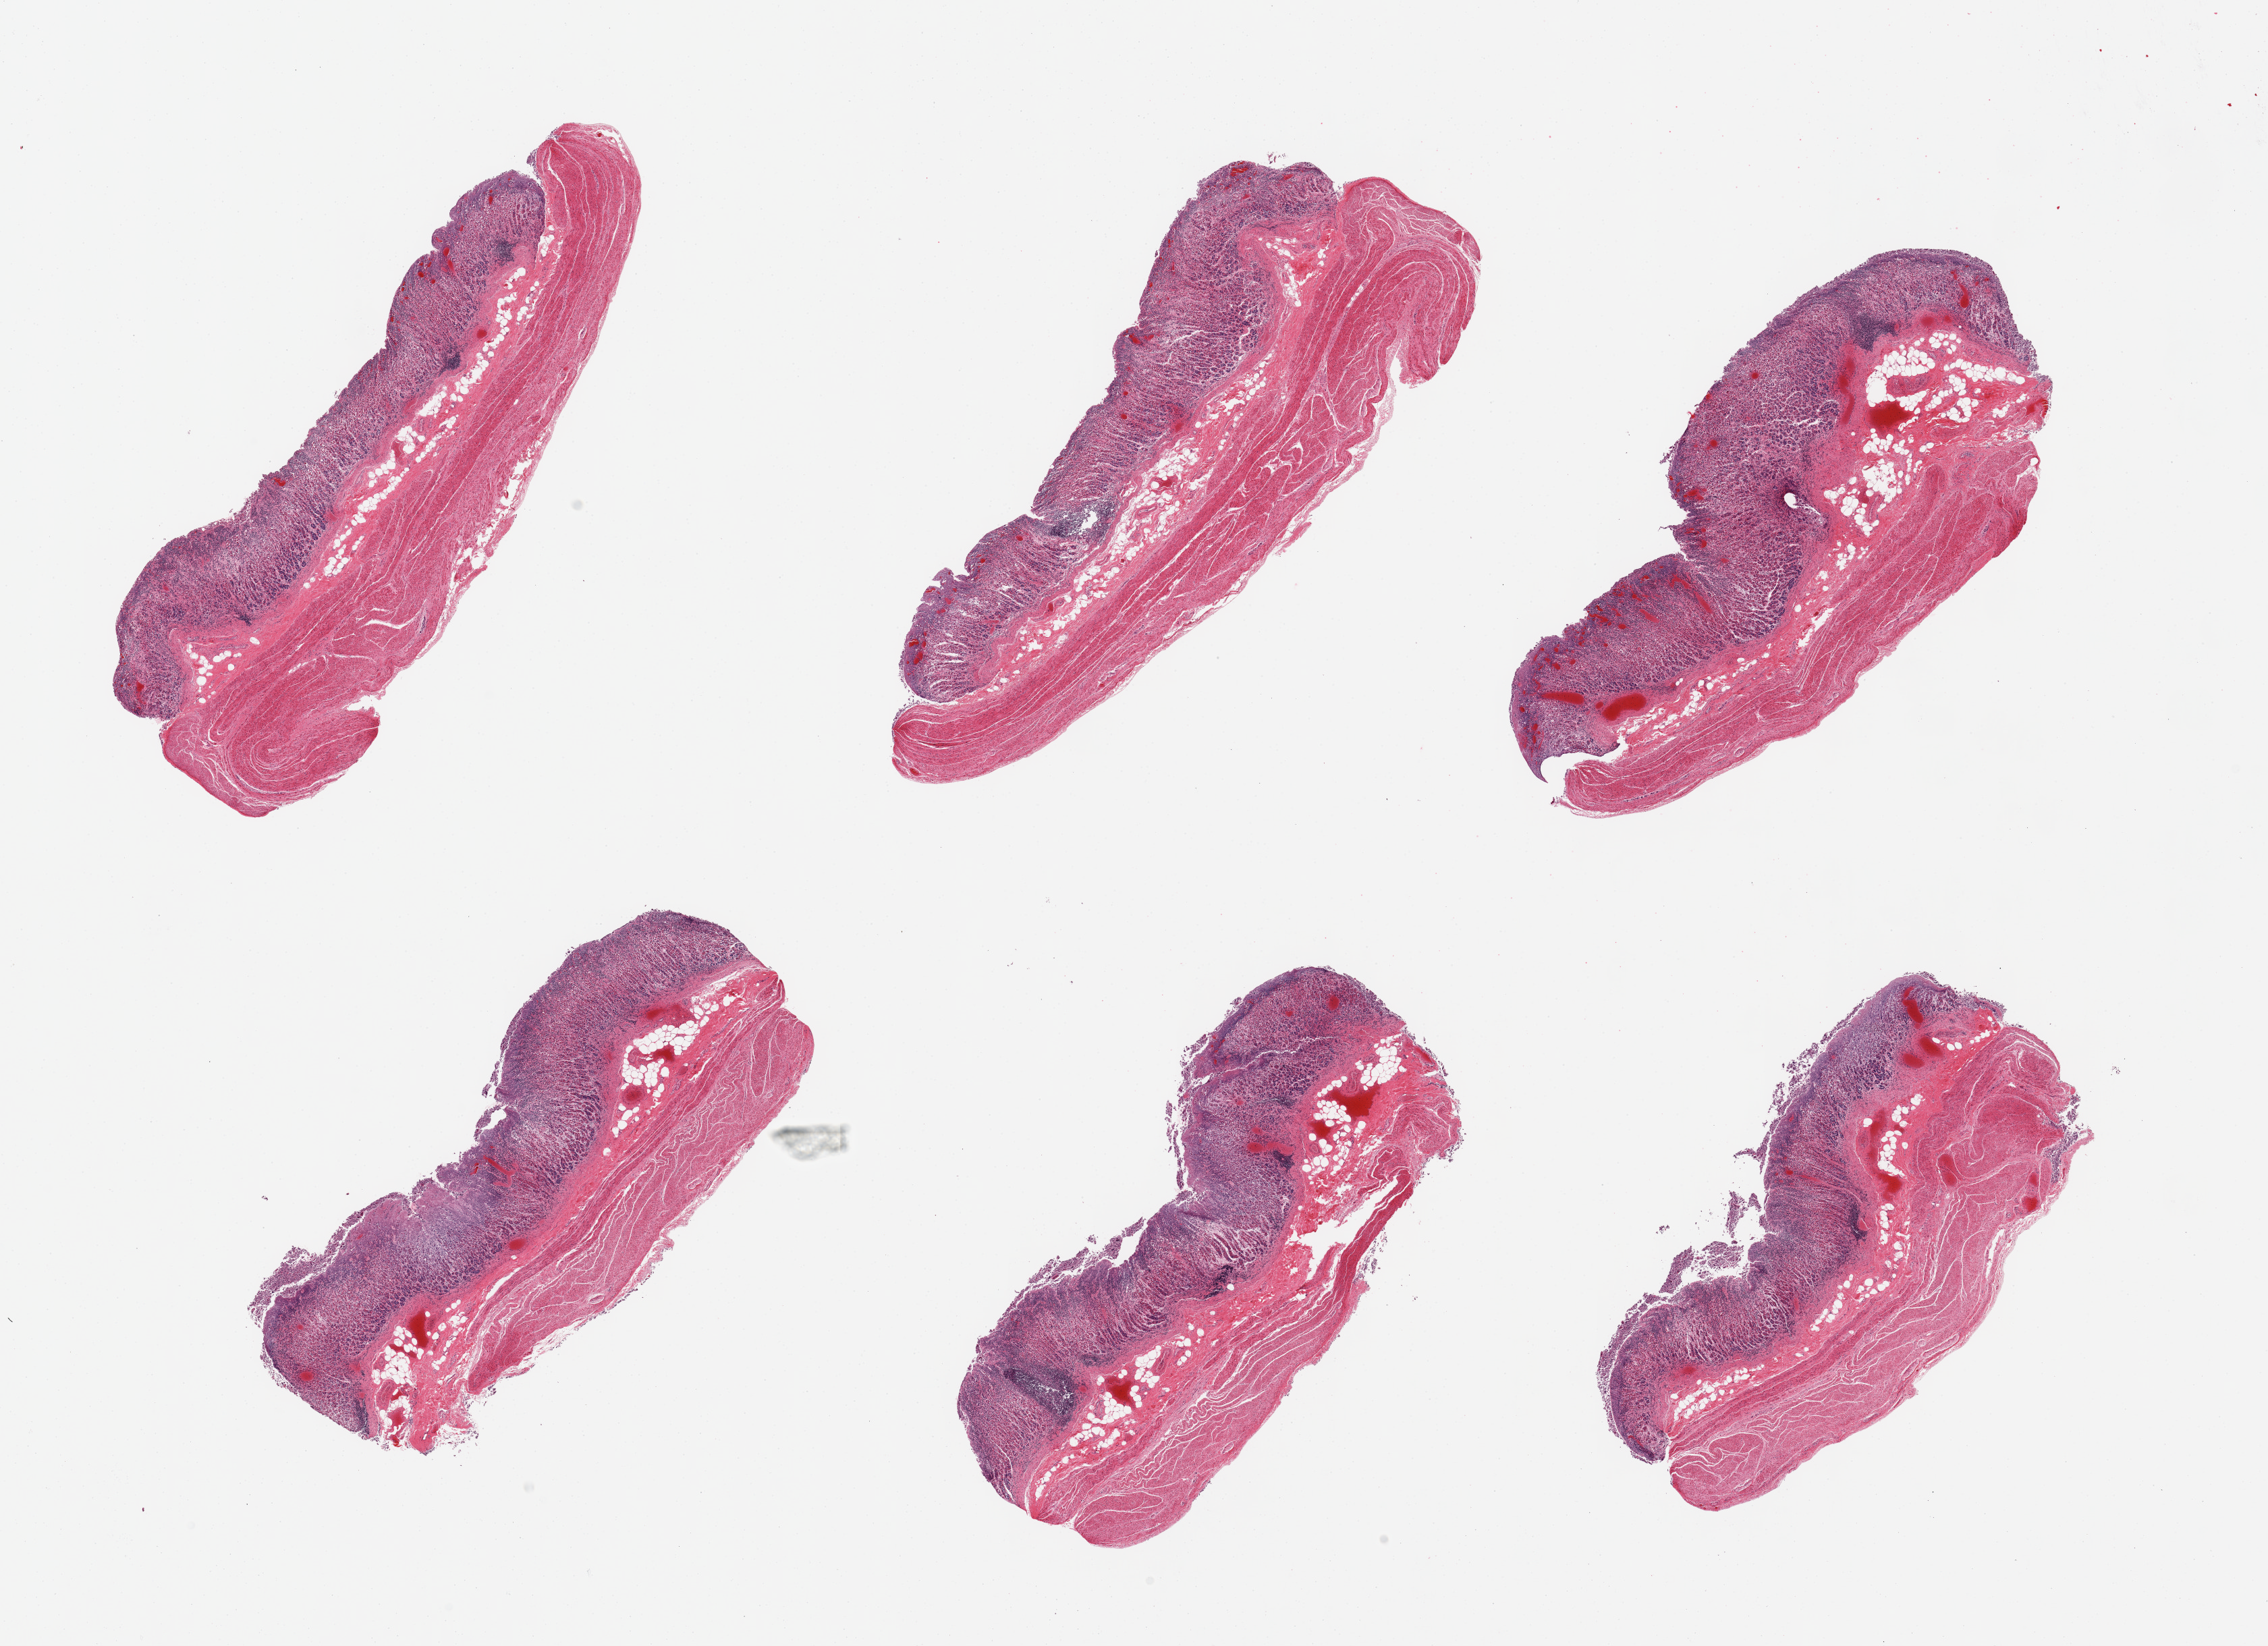
Digitized hematoxylin and eosin (H&E)-stained section, brightfield — whole scanned area (about 26.6 x 19.3 mm, from a 20x scan) shown as a low-resolution overview; PAXgene-fixed paraffin-embedded (PFPE) section; target tissue: stomach; tissue donor sample. Donor: male.
Pathologist's review note for this sample: 6 pieces; chronic gastritis; mucosa largely autolyzed.